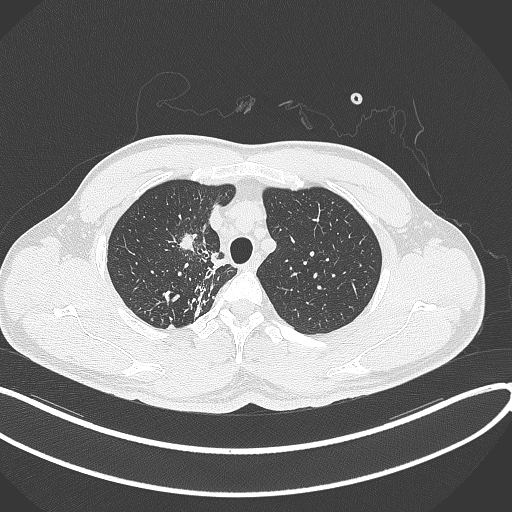
Chest CT, one axial slice. Slice 304 of 391 in the series (ordered by position). Reconstruction kernel B70f. 120 kVp. Lung window (W 1500 / L -600 HU). 1 mm slice thickness. 512 × 512 image matrix. Patient: male, 48 years. From the clinical record (not read from this slice): clinical TNM (as recorded): T1c N1 M1.
Annotated regions visible in this slice (bounding box drawn by a radiologist):
- lung tumour (recorded histology: adenocarcinoma): bounding box (x1, y1, x2, y2) in pixels: (175, 228, 204, 257)